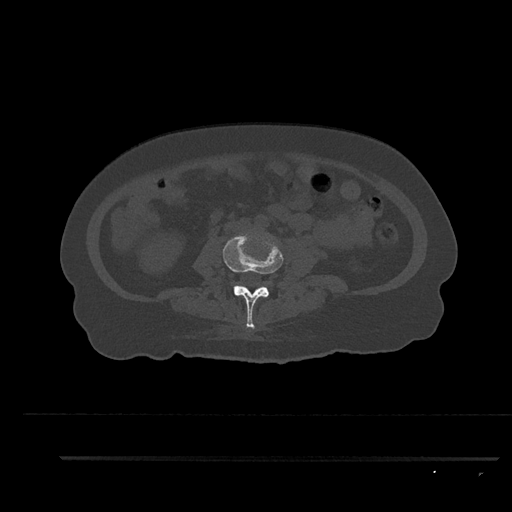
CT including the spine, one axial slice; position 70 of 797 along the scan axis; reconstruction kernel Br40s/3; bone window (W 1800 / L 400 HU); 0.5 mm slice thickness; 512 × 512 image matrix, field of view 408 × 408 mm. Female patient, age 44 years. From the clinical record (not read from this slice): primary cancer: renal; vertebrae with lytic lesions (as recorded): L1.
Annotated regions visible in this slice (semi-automatically segmented with operator editing):
- L3 vertebra: bounding box [x1, y1, x2, y2] px = [223, 233, 284, 329]